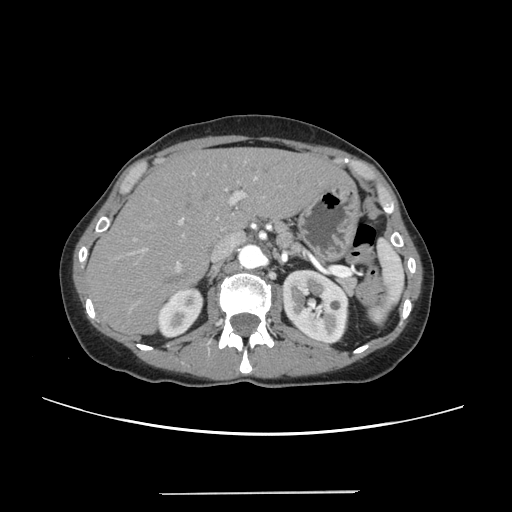
Contrast-enhanced abdominal CT, one axial slice; slice 159 of 240 in the series (ordered by position); 120 kVp; intravenous contrast given; soft-tissue window (W 400 / L 40 HU); 1.25 mm slice thickness; 512 × 512 image matrix. Female patient, age 60 years. From the clinical record (not read from this slice): diagnosis: colorectal cancer liver metastases, imaged before liver resection; multiple liver metastases: no; largest metastasis: 1.5 cm; disease in both lobes: no.
Structures marked on this image (outlined manually by an expert reader):
- liver: box from (x=88, y=148) to (x=348, y=334) px
- planned liver remnant (the part of the liver to remain after resection): (x=88, y=148)–(x=347, y=333)
- portal vein (with intrahepatic branches): (x=141, y=171)–(x=259, y=271)